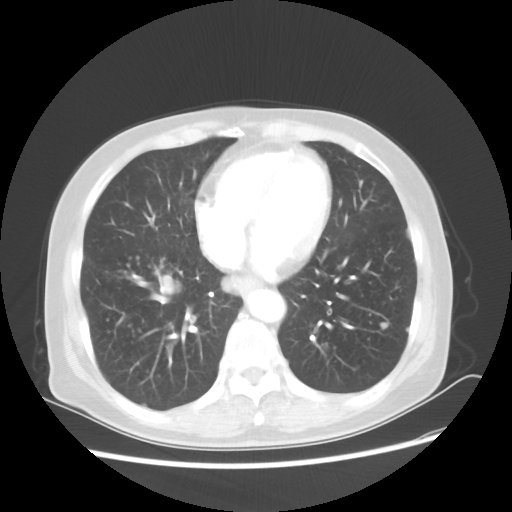
Chest CT, one axial slice. Position 19 of 56 along the scan axis. 80 kVp. Lung window (W 1500 / L -600 HU). 5 mm slice thickness. 512 × 512 image matrix, field of view 360 × 360 mm. Female patient, age 68 years. From the clinical record (not read from this slice): clinical TNM (as recorded): T1c N3 M0.
Outlined on this slice (rectangle marked by the reading radiologist):
- lung tumour (recorded histology: squamous cell carcinoma): bounding box (x1, y1, x2, y2) in pixels: (151, 271, 192, 309)